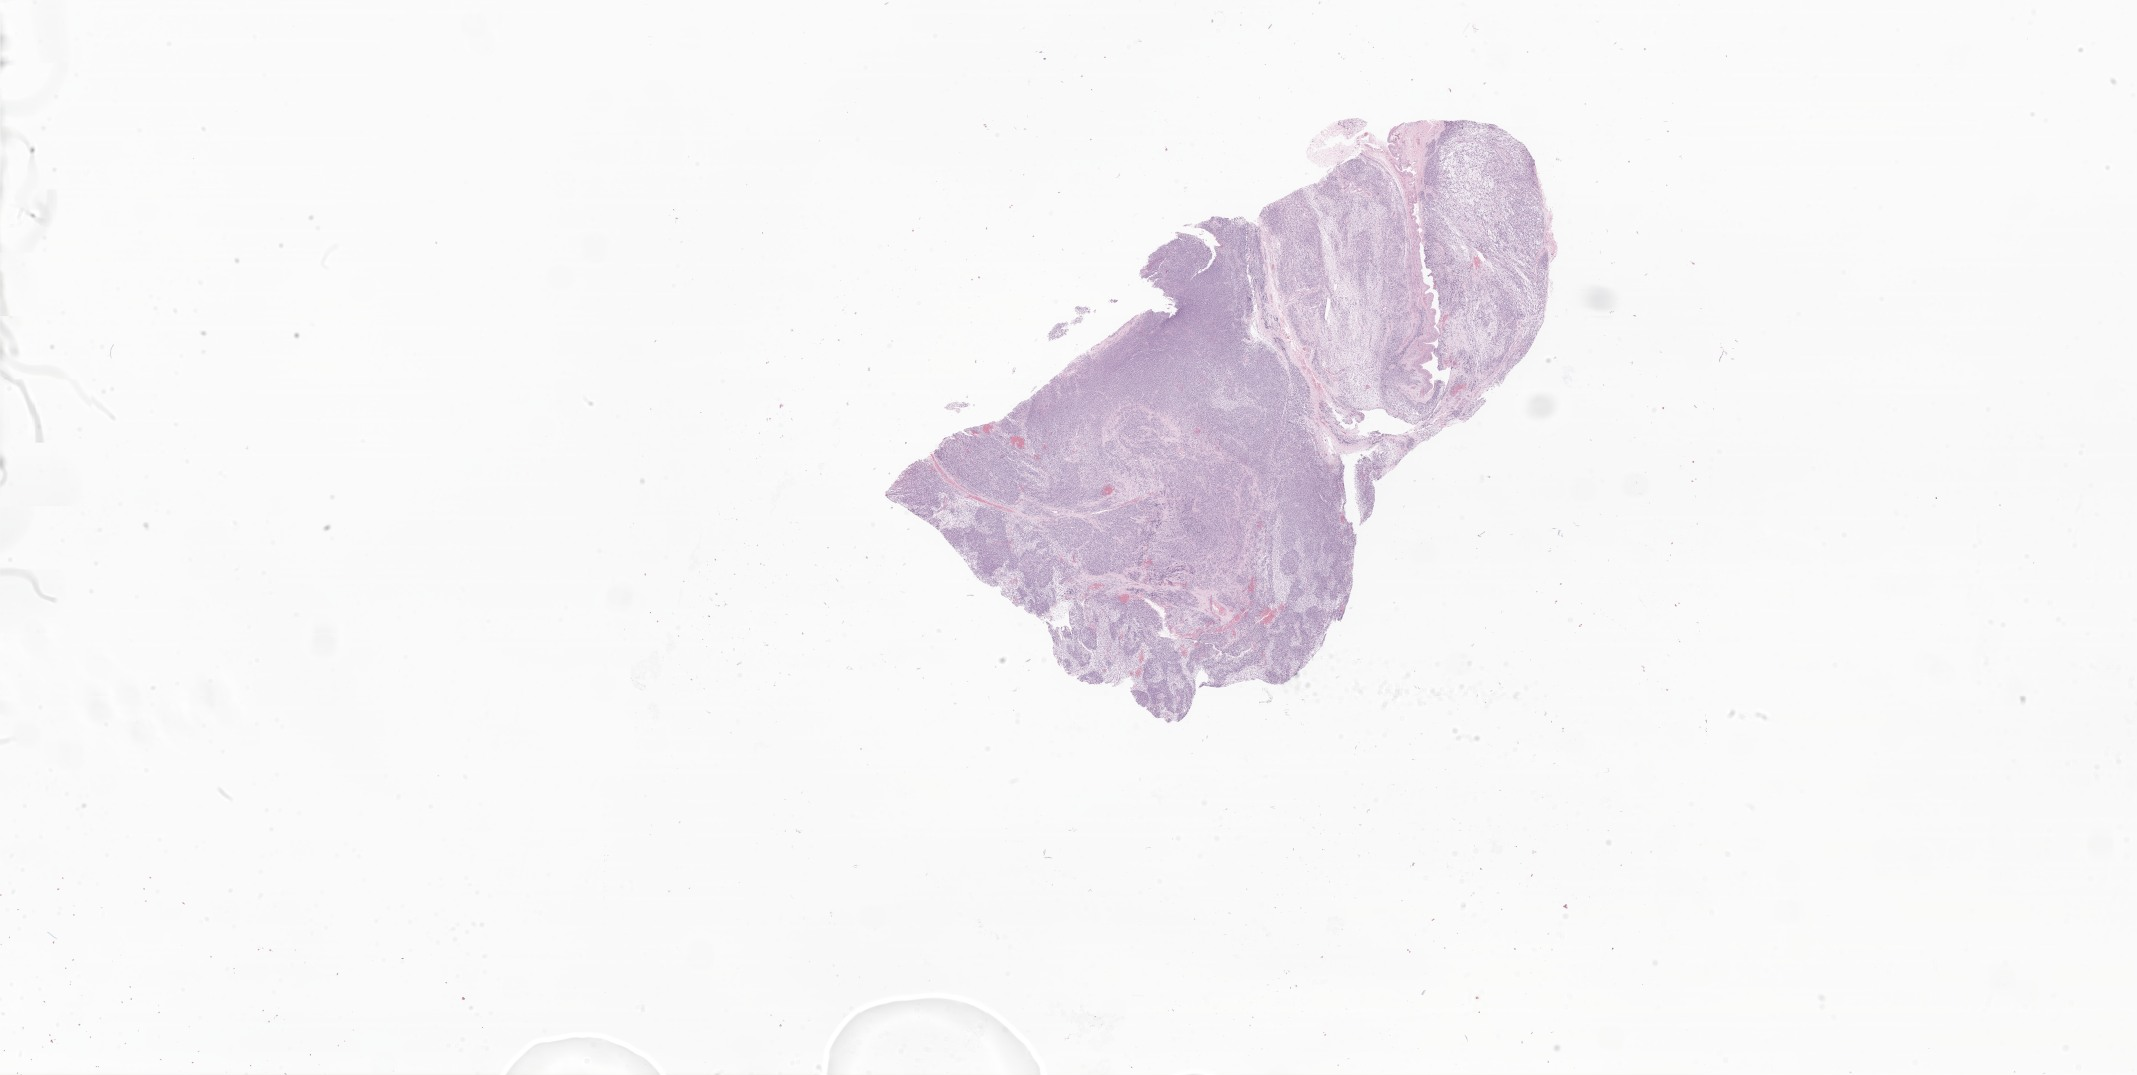
Digitized haematoxylin and eosin-stained section of tumor tissue from the orbit, low-resolution overview of the scanned area, about 36.0 x 18.1 mm; formalin-fixed, paraffin-embedded (FFPE) tissue. Patient male; age 68 months (5 years 8 months).
Diagnosis (ICD-O-3 morphology term): Embryonal rhabdomyosarcoma, NOS.